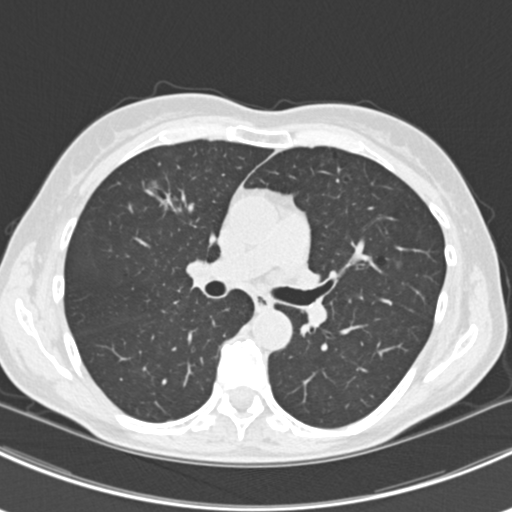
Axial slice from a low-dose chest CT screening exam, first (baseline) screen, lung window (W 1500 / L -600 HU), 2 mm slice thickness, 120 kVp, slice 78 of 224 in the series. Female, age 63 years at enrolment. Current smoker at enrolment.
Lesion marked by an expert reader, bounding box <145,175,201,230> (left, top, right, bottom; pixels). The screening reader recorded 10 non-calcified nodules or masses ≥4 mm on this exam; which of them this box marks is not recorded. Official screen result: positive, change unspecified: nodule(s) >= 4 mm or enlarging nodule(s), mass(es), or other non-specific abnormalities suspicious for lung cancer. Later outcome: lung cancer diagnosed 751 days after this screen (after the third annual screen) — bronchiolo-alveolar adenocarcinoma, NOS, right upper lobe, right middle lobe, right lower lobe, left upper lobe, left lower lobe, moderately differentiated (G2), stage IV (AJCC 6th edition).